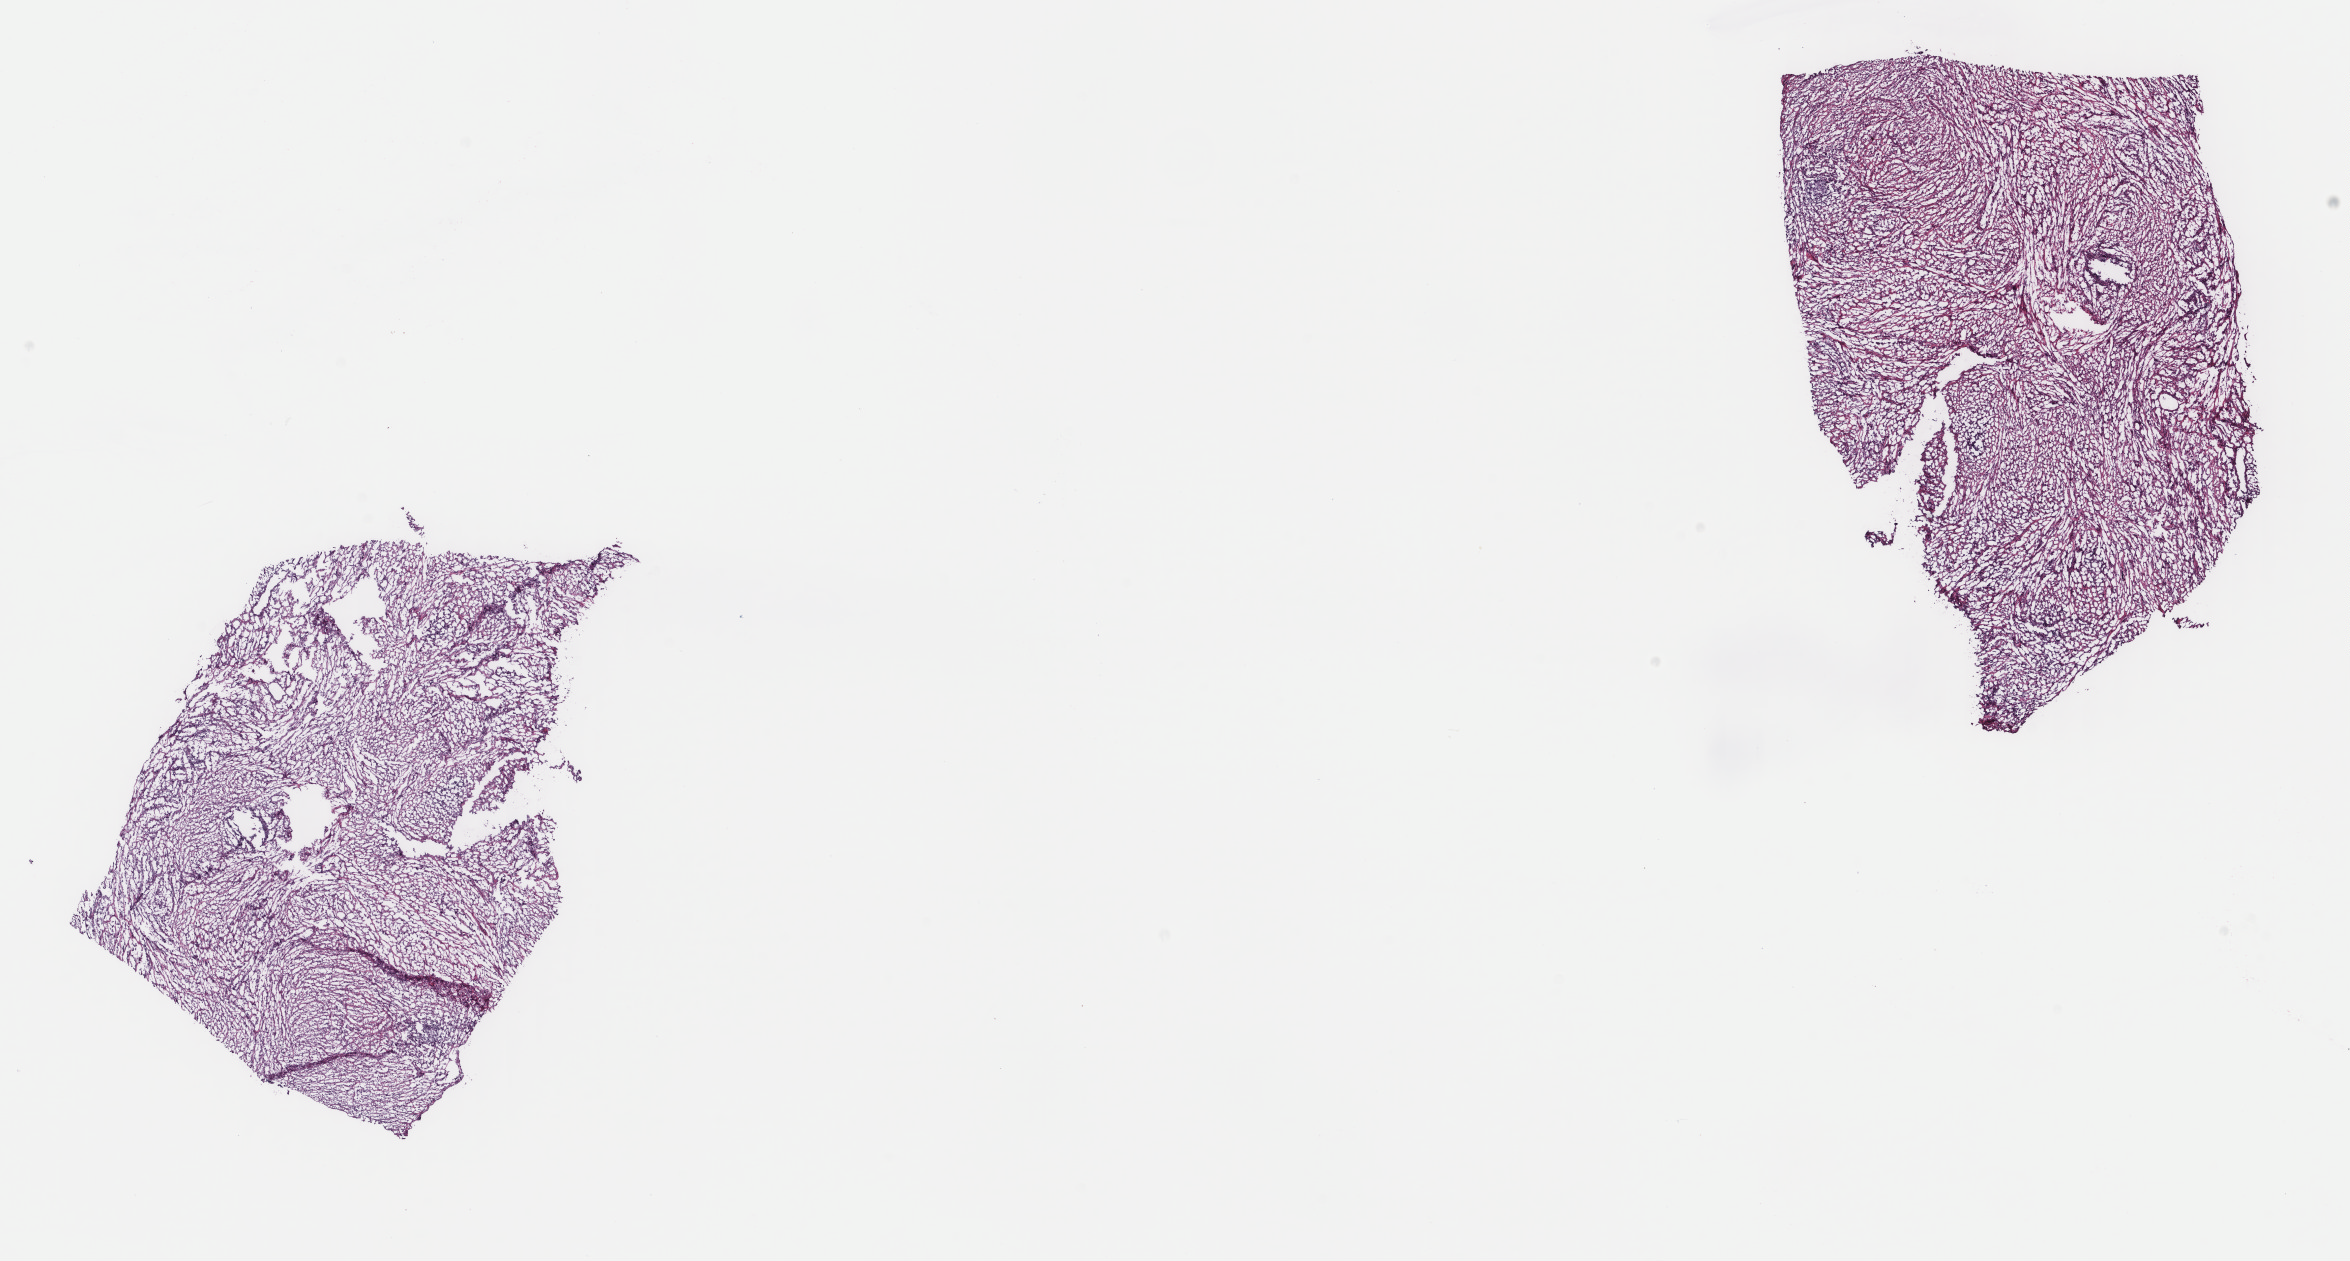
Whole-slide histology image, H&E — a low-resolution overview of the entire scanned area, about 18.7 x 10.0 mm (from a 40x scan); frozen section from the top of the tissue portion; sample: primary tumour, skin. Male, age 77 years at initial diagnosis. Composition of this section per pathologist review: tumour cells 70%, tumour nuclei 70%, normal cells 0%, stromal cells 30%, necrosis 0%. Inflammatory infiltration, as recorded: lymphocyte infiltration 6%, monocyte infiltration 1%, neutrophil infiltration 1%.
Histologic diagnosis: Spindle cell melanoma, NOS.